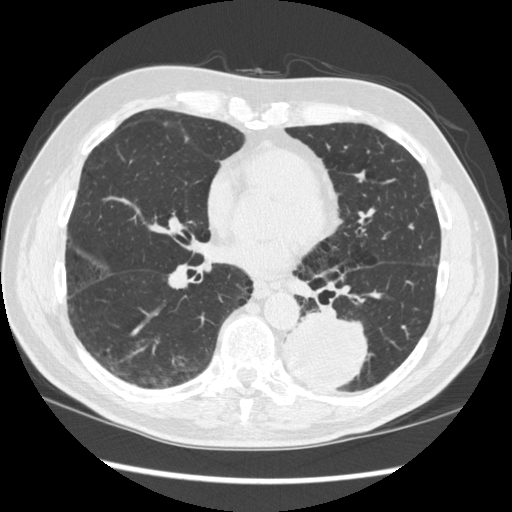
Low-dose screening chest CT, axial slice; baseline screening round; lung window (W 1500 / L -600 HU); 1.25 mm slice thickness; standard (soft-tissue) reconstruction kernel (STANDARD); 120 kVp; slice 148 of 348 in the series. Male participant, aged 72 years at enrolment. Current smoker at enrolment.
Expert reader's lesion annotation, box from (x=268, y=302) to (x=372, y=393) px. The screening reader recorded 2 non-calcified nodules or masses ≥4 mm on this exam; which of them this box marks is not recorded. Later outcome: lung cancer diagnosed 37 days after this screen — squamous cell carcinoma, NOS, left lower lobe, stage IIIA (AJCC 6th edition), 60 mm at pathology.